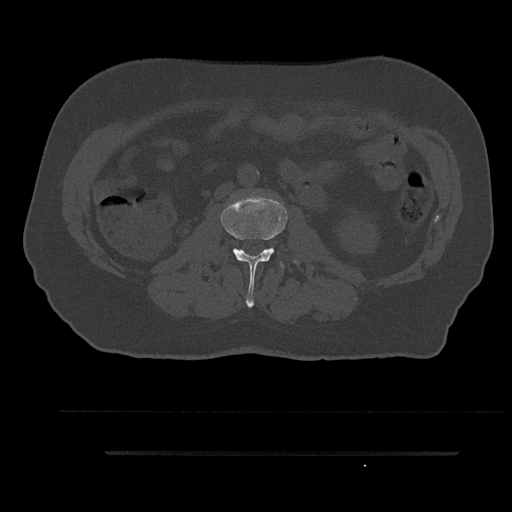
CT including the spine, one axial slice. Position 96 of 797 along the scan axis. 120 kVp. Bone window (W 1800 / L 400 HU). 512 × 512 image matrix, field of view 432 × 432 mm. Male patient, age 63 years. Case-level facts recorded for this patient, not image findings: primary cancer: renal.
Structures marked on this image (semi-automatic segmentation, software-assisted and operator-edited):
- L2 vertebra: bounding box [x1, y1, x2, y2] px = [221, 195, 298, 308]